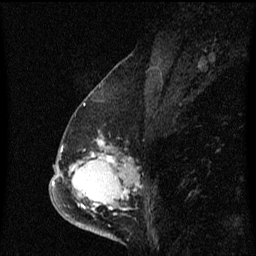
Breast MRI (dynamic contrast-enhanced), one sagittal slice; position 29 of 60 along the scan axis; dynamic contrast-enhanced series, image 2 of 3 at this slice position (ordered by acquisition); 1.5 T; TE 4.2 ms, TR 8.4 ms; 2 mm slice thickness; 256 × 256 image matrix. Female patient, age 57 years. Case-level facts recorded for this patient, not image findings: setting: breast cancer imaged before/during neoadjuvant chemotherapy; receptor status: HR-positive, HER2-negative.
Structures marked on this image (semi-automatic segmentation, software-assisted and operator-edited):
- analysis volume of interest (the breast-tissue region the enhancement analysis was run in; not a lesion): bounding box <66,130,129,177> (left, top, right, bottom; pixels)
- tumour enhancement mask (voxels above the 70 % enhancement threshold inside the analysis volume of interest): <97,140,112,163>